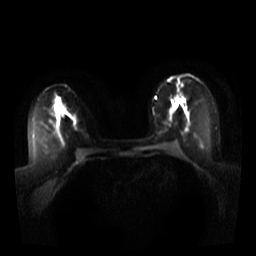
Breast MRI, one axial slice. Slice 17 of 44 in the series (ordered by position). Diffusion-weighted series; image 2 of 4 stored at this slice position (different b-values; order by instance number). 3 T. 256 × 256 image matrix, field of view 340 × 340 mm. Female patient.
Outlined on this slice (outlined manually by an expert reader):
- tumour on diffusion-weighted imaging: bounding box [x1, y1, x2, y2] px = [175, 104, 177, 108]